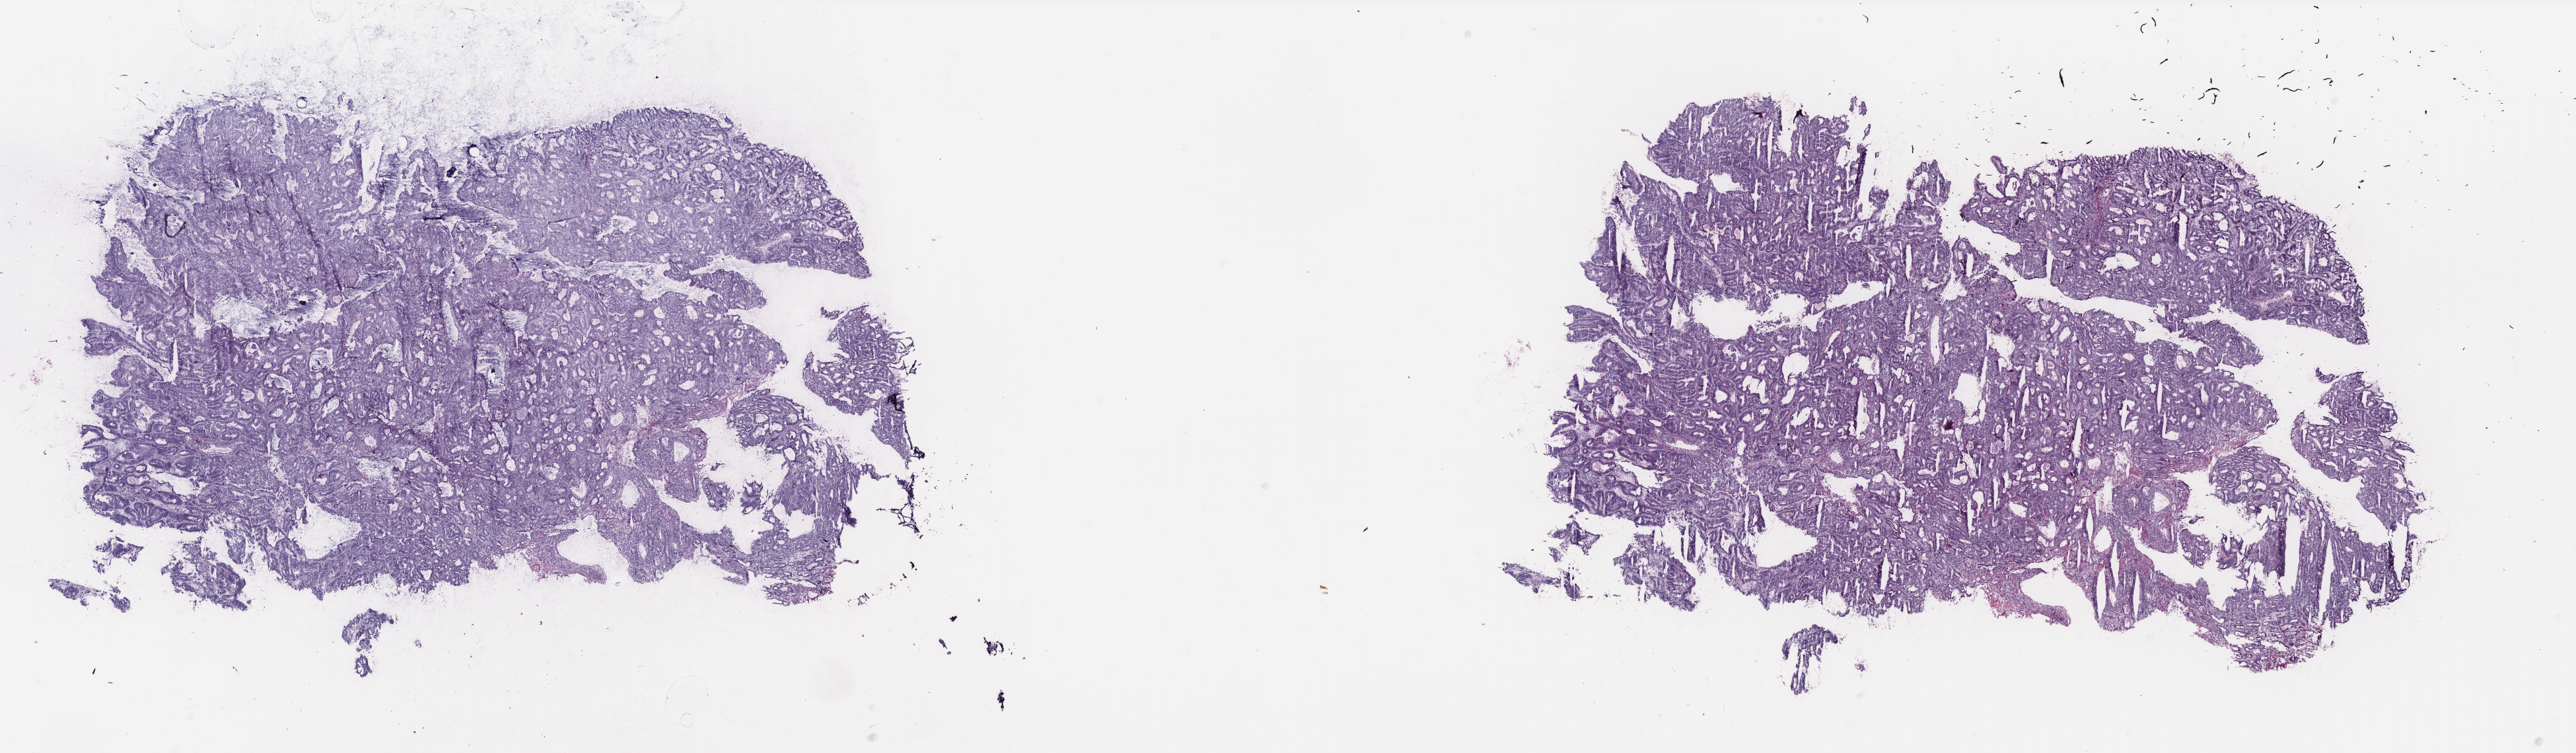
H&E whole-slide image — a low-resolution overview of the entire scanned area, about 31.3 x 9.1 mm (from a 40x scan); frozen section; primary tumour sample from the uterus. Patient: female, age at initial diagnosis 60 years.
Pathologic diagnosis: Endometrioid adenocarcinoma, NOS (endometrium).